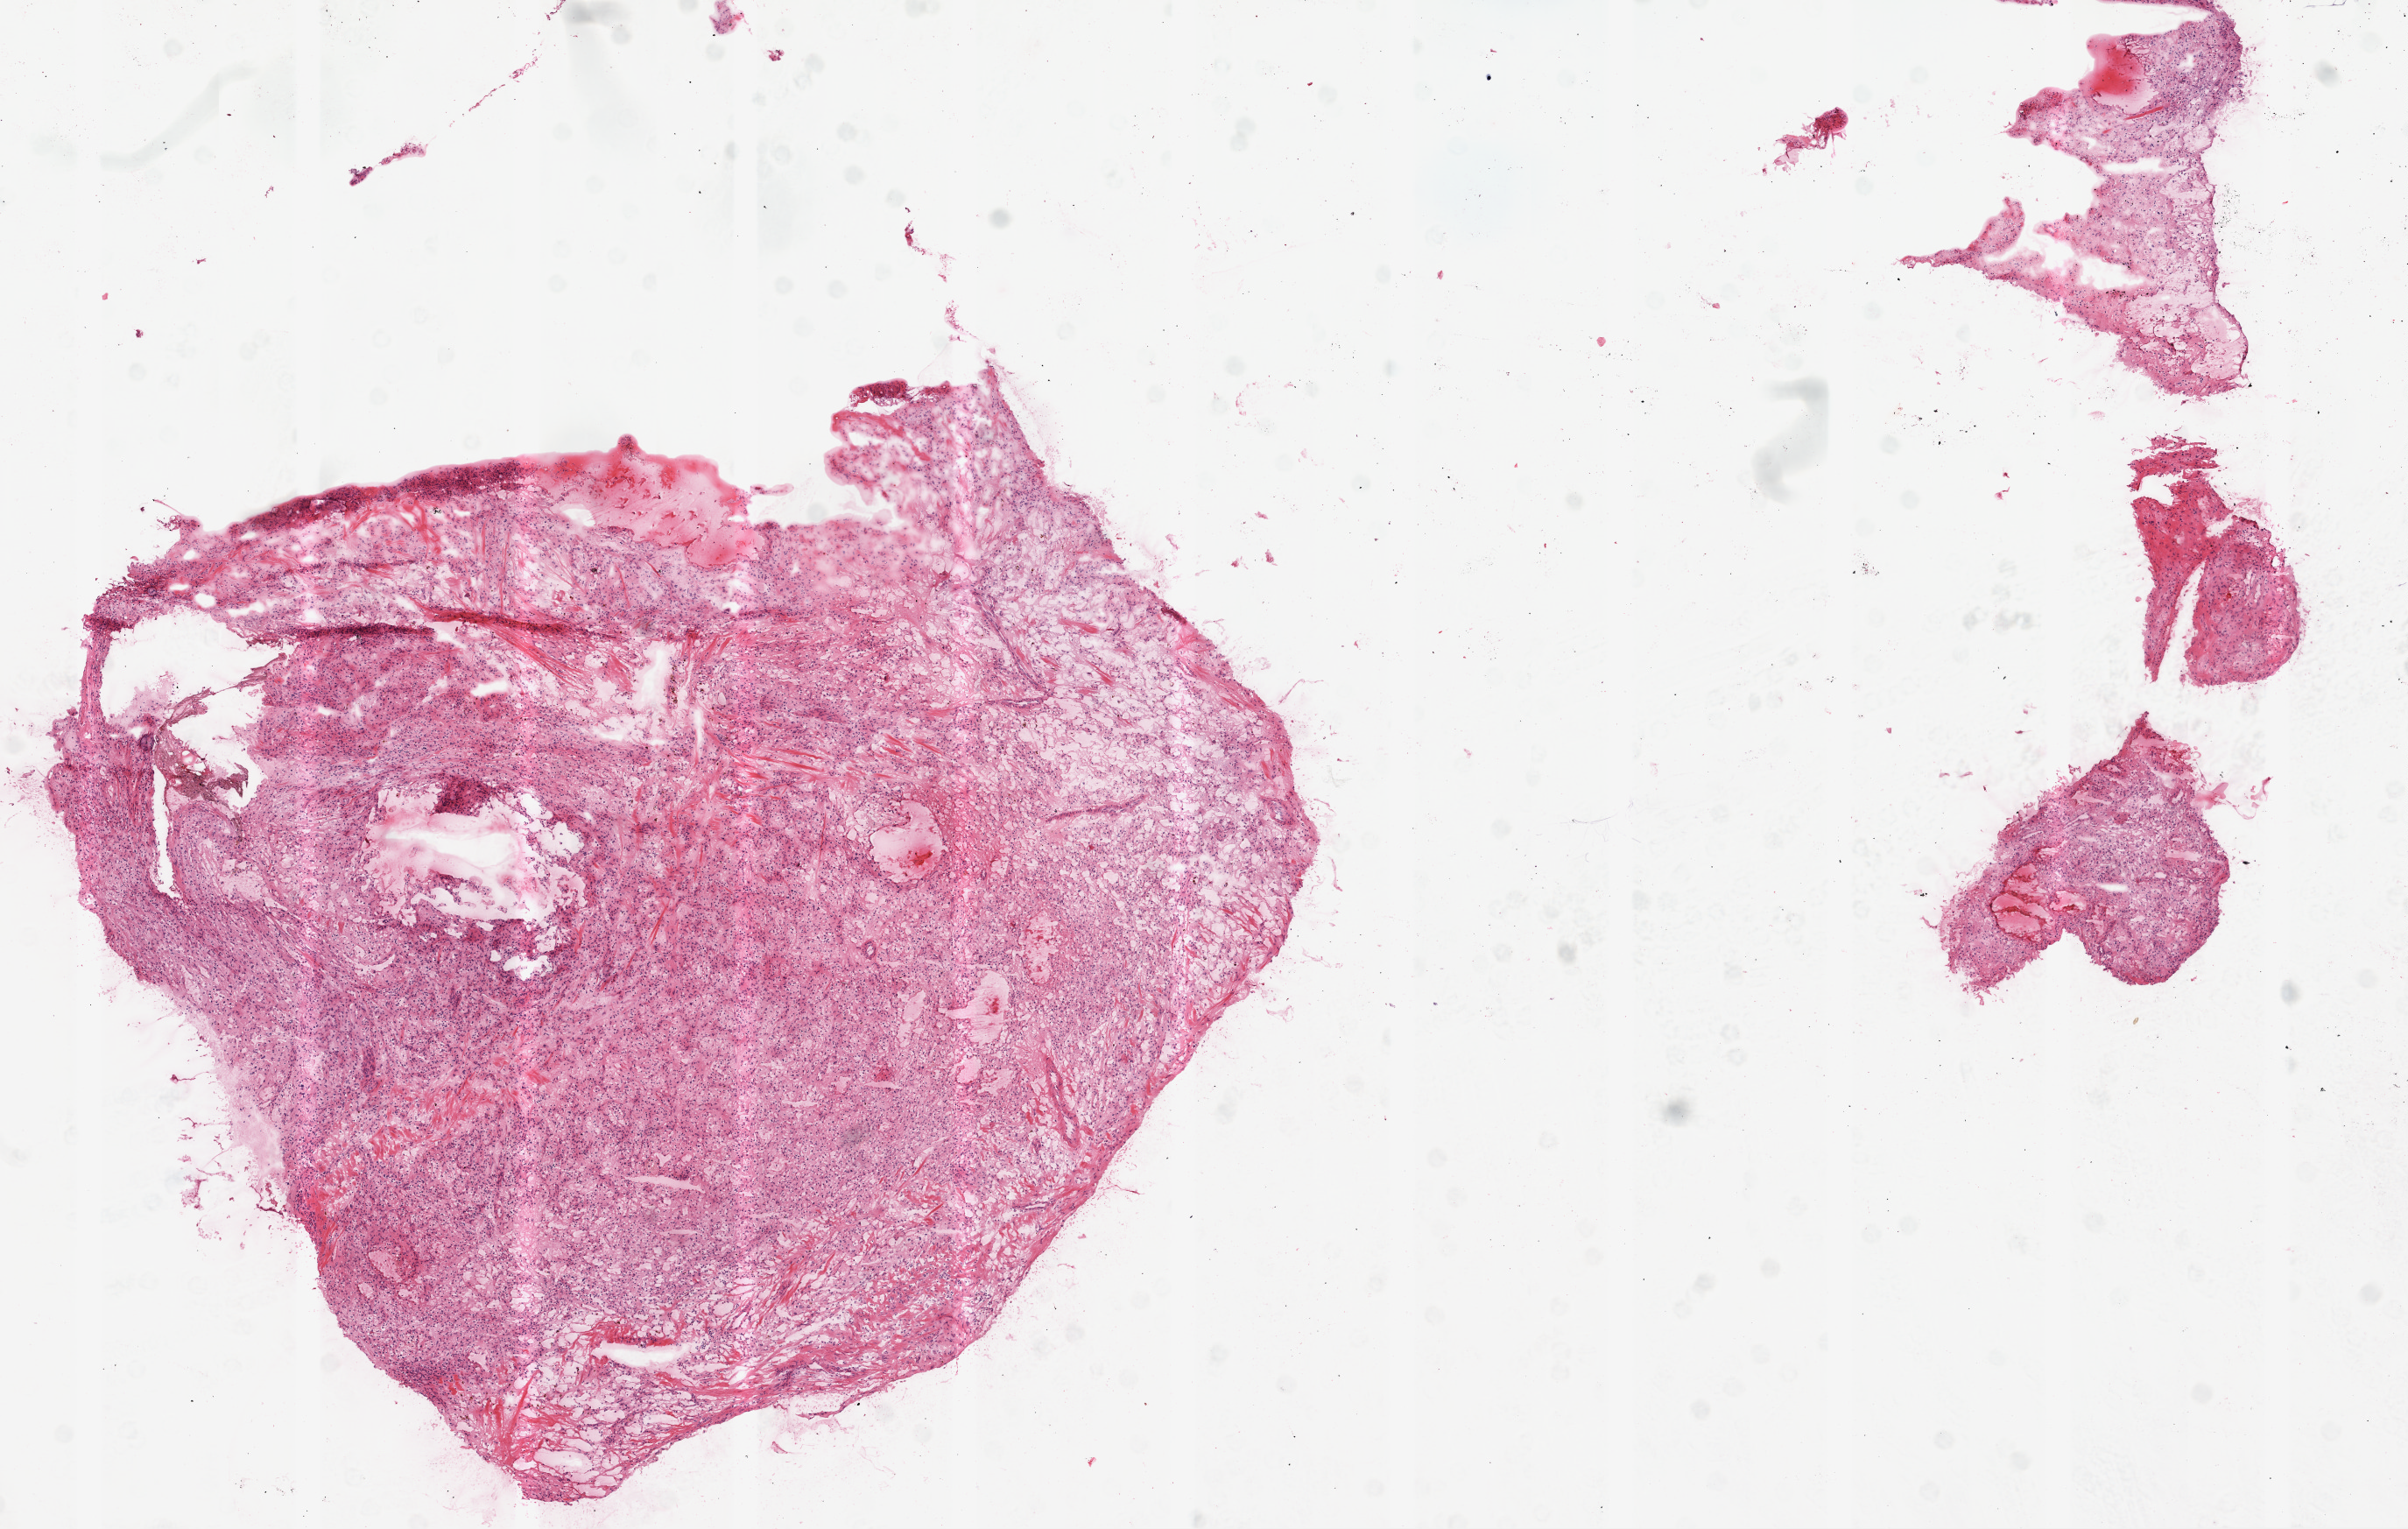
Whole-slide histology image, Hematoxylin and eosin (H&E) stained — low-resolution overview of the scanned area, about 11.0 x 7.0 mm, frozen section from the top of the tissue portion, kidney, primary tumour sample. Patient: female, age at initial diagnosis 72 years. Histologic grade: G2 (moderately differentiated). Slide review estimates, as recorded: tumour cells 90%, tumour nuclei 85%, normal cells 0%, stromal cells 10%, necrosis 0%.
Pathologic diagnosis: Clear cell adenocarcinoma, NOS. Laterality: left. TNM: T1a N0 M0. AJCC pathologic stage: I (7th edition).